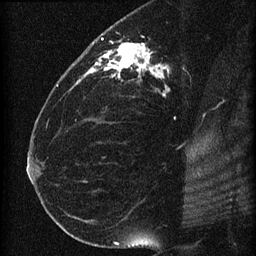
Breast MRI (dynamic contrast-enhanced), one sagittal slice; dynamic contrast-enhanced series, image 2 of 4 at this slice position (ordered by acquisition); 1.5 T; TE 4.2 ms, TR 22.7 ms; 1.5 mm slice thickness; 256 × 256 image matrix, field of view 180 × 180 mm. Female patient, age 35 years. Case-level facts recorded for this patient, not image findings: setting: breast cancer imaged before/during neoadjuvant chemotherapy; receptor status: HR-positive, HER2-negative.
Annotated regions visible in this slice (semi-automatically segmented with operator editing):
- analysis volume of interest (the breast-tissue region the enhancement analysis was run in; not a lesion): bounding box <69,27,199,112> (left, top, right, bottom; pixels)
- tumour enhancement mask (voxels above the 90 % enhancement threshold inside the analysis volume of interest): <76,37,169,95>